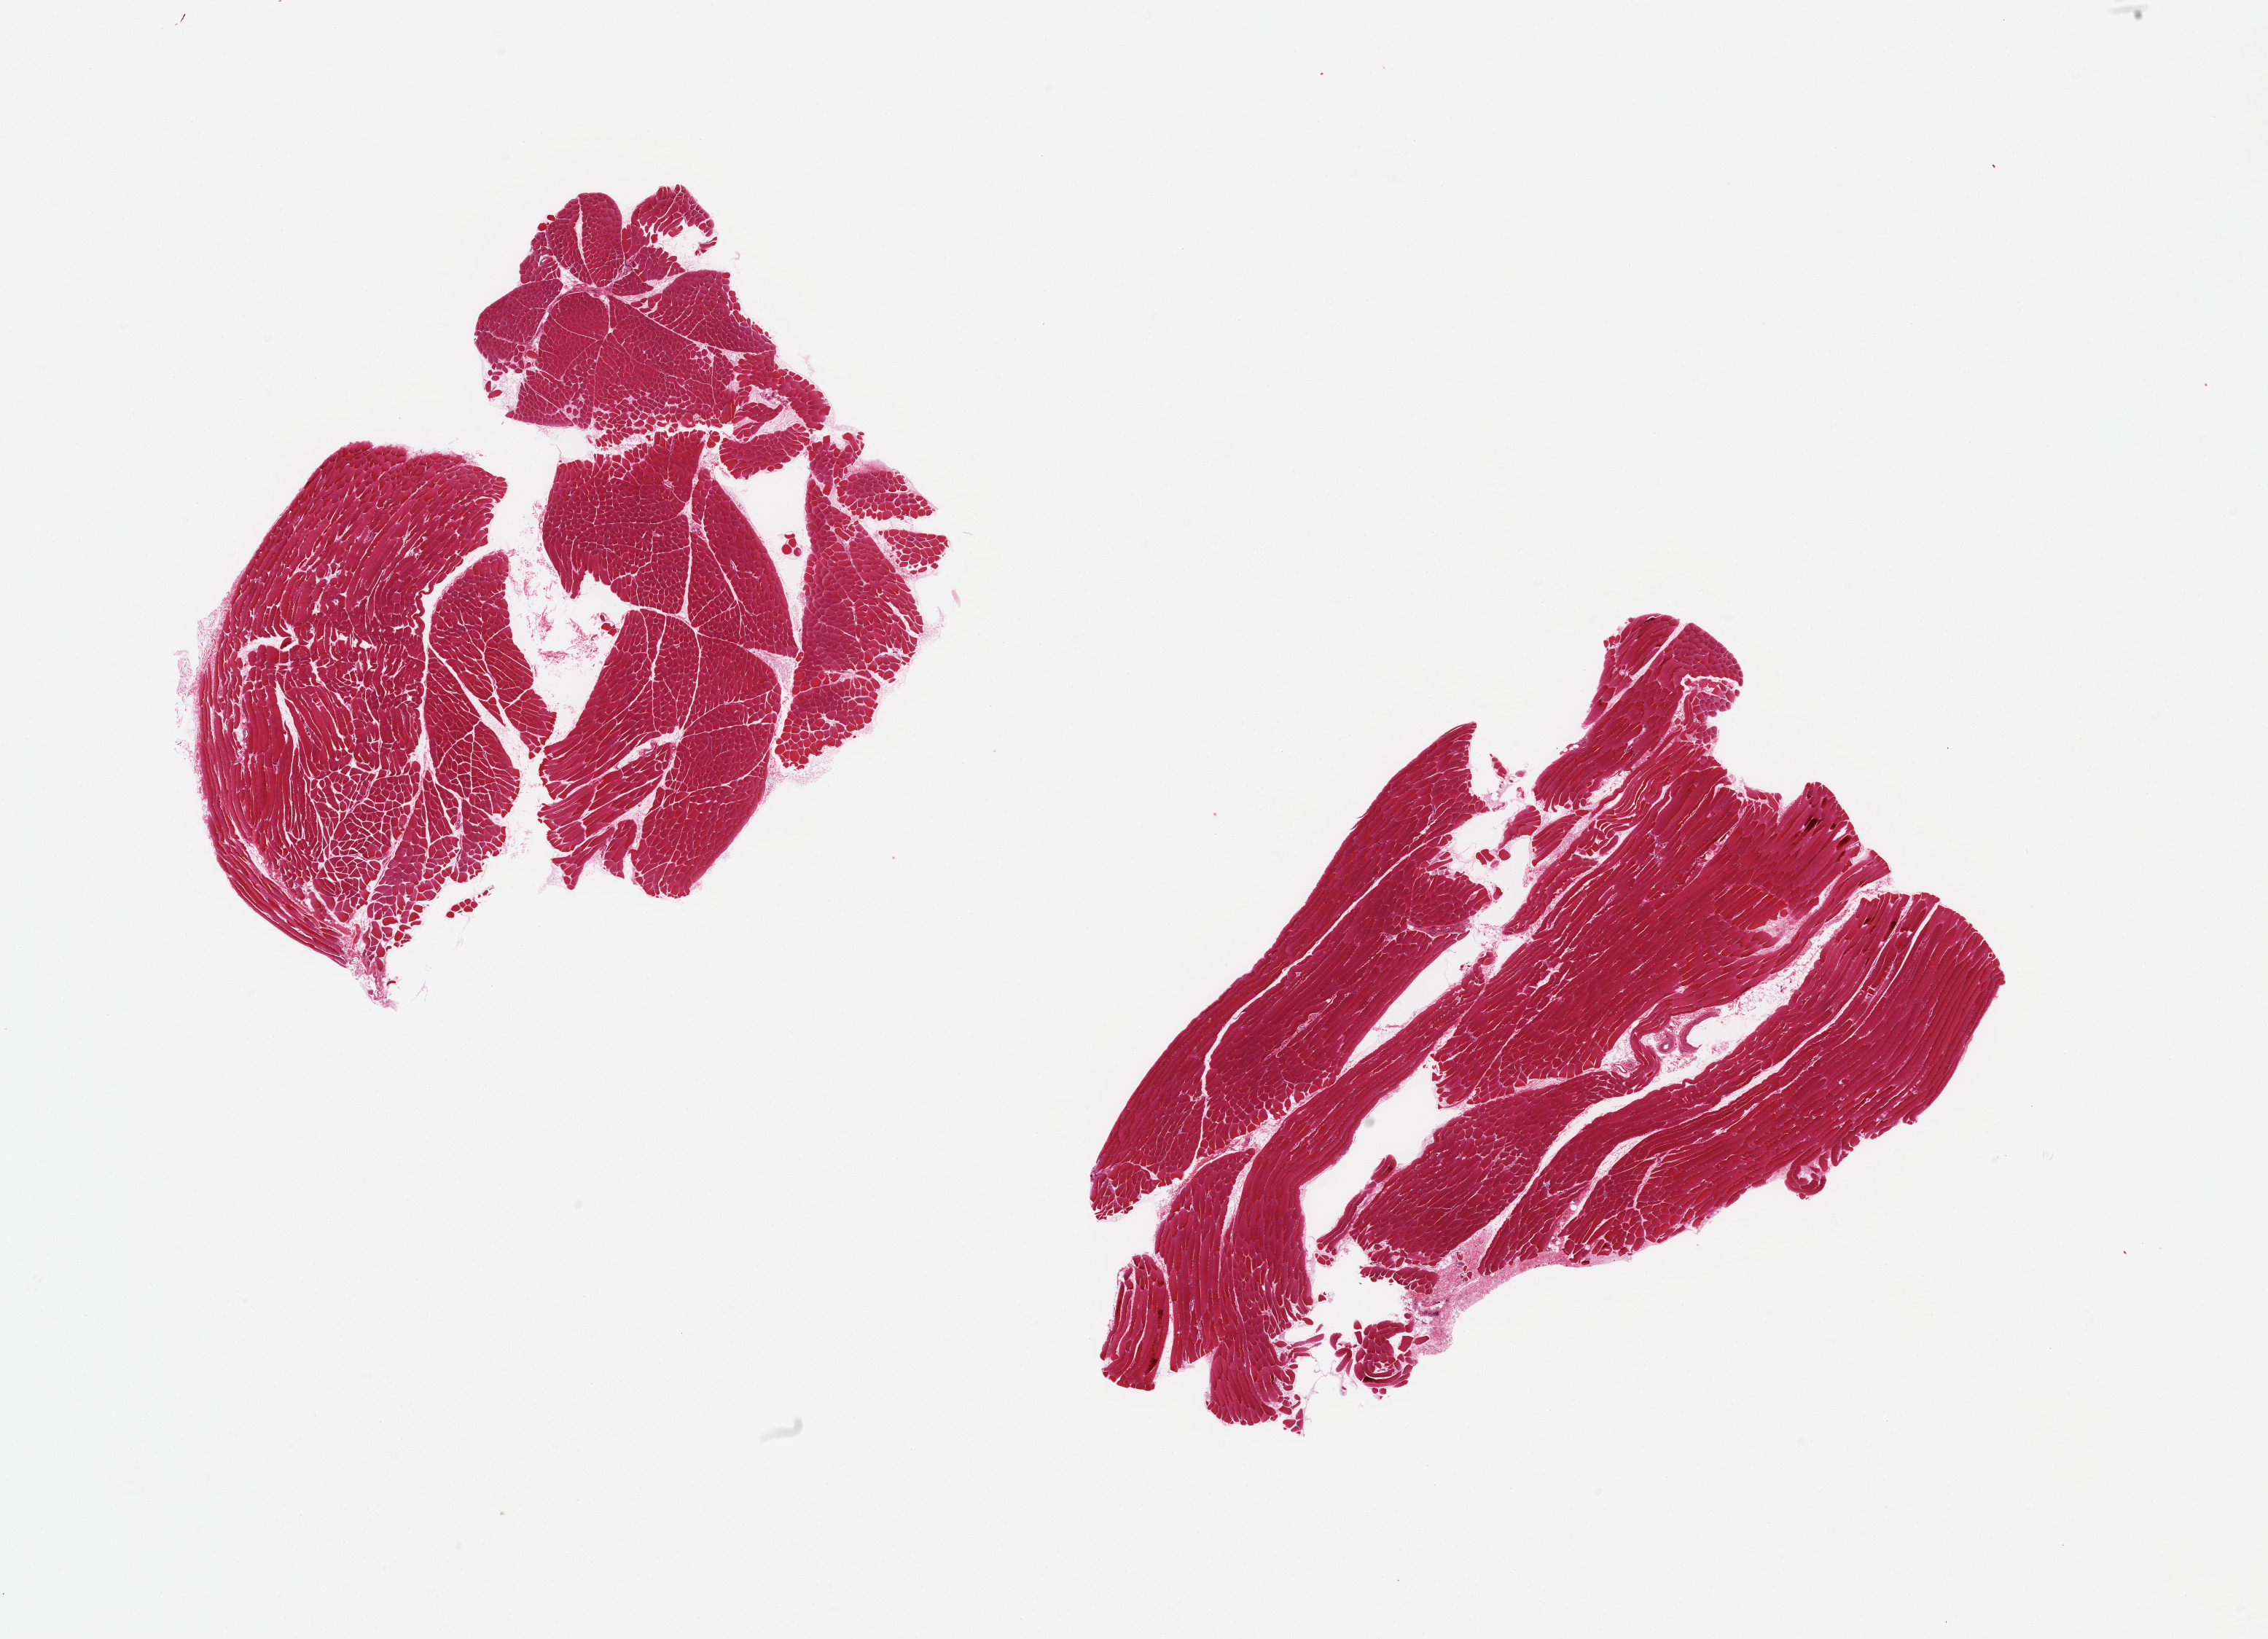
Whole-slide image, hematoxylin and eosin (H&E) stain — whole scanned area (about 24.6 x 17.8 mm) shown as a low-resolution overview. PAXgene-fixed paraffin-embedded (PFPE) section. Target tissue: skeletal muscle. Tissue donor sample.
Reviewer comment on this tissue sample: 2 pieces; ~20% washed off internal fat (empty spaces).